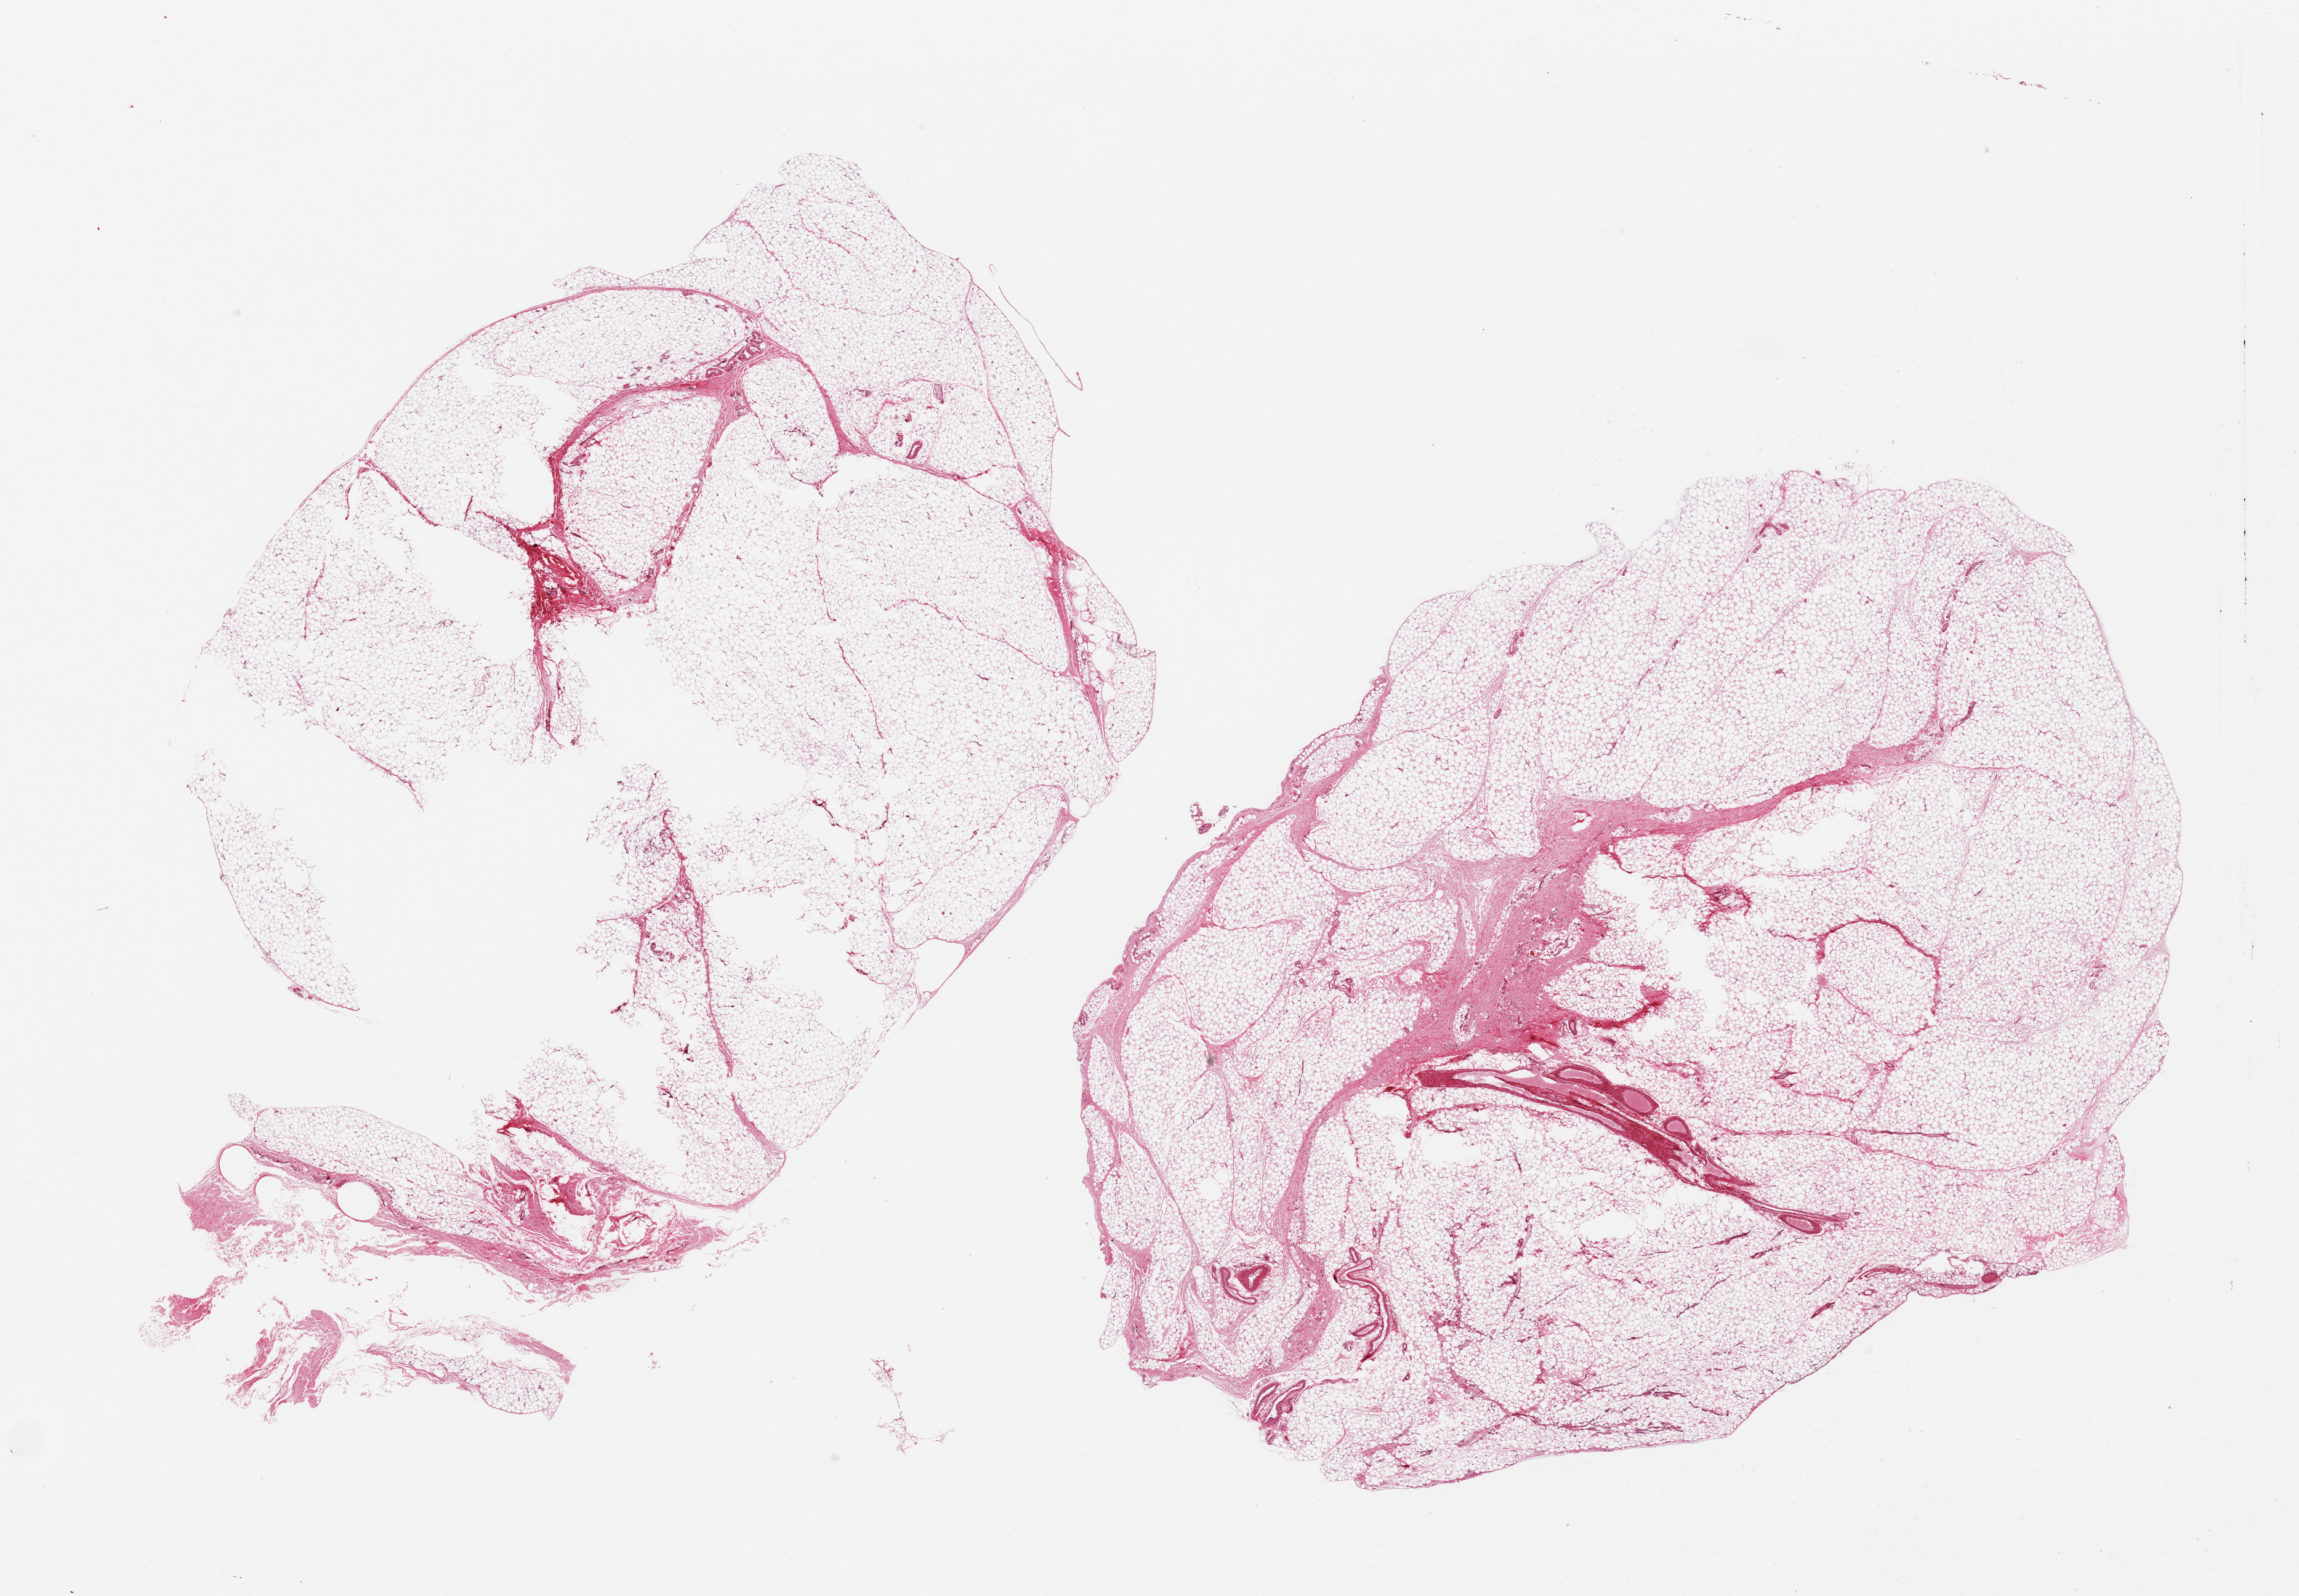
Digitized haematoxylin and eosin-stained section, low-resolution overview of the scanned area, about 29.5 x 20.5 mm. PAXgene-fixed paraffin-embedded (PFPE) section. Section of omentum (target tissue). Tissue donor sample.
- reviewer comment on this tissue sample: 2 pieces; extraneous and/or foreign material in 1 piece, <10%